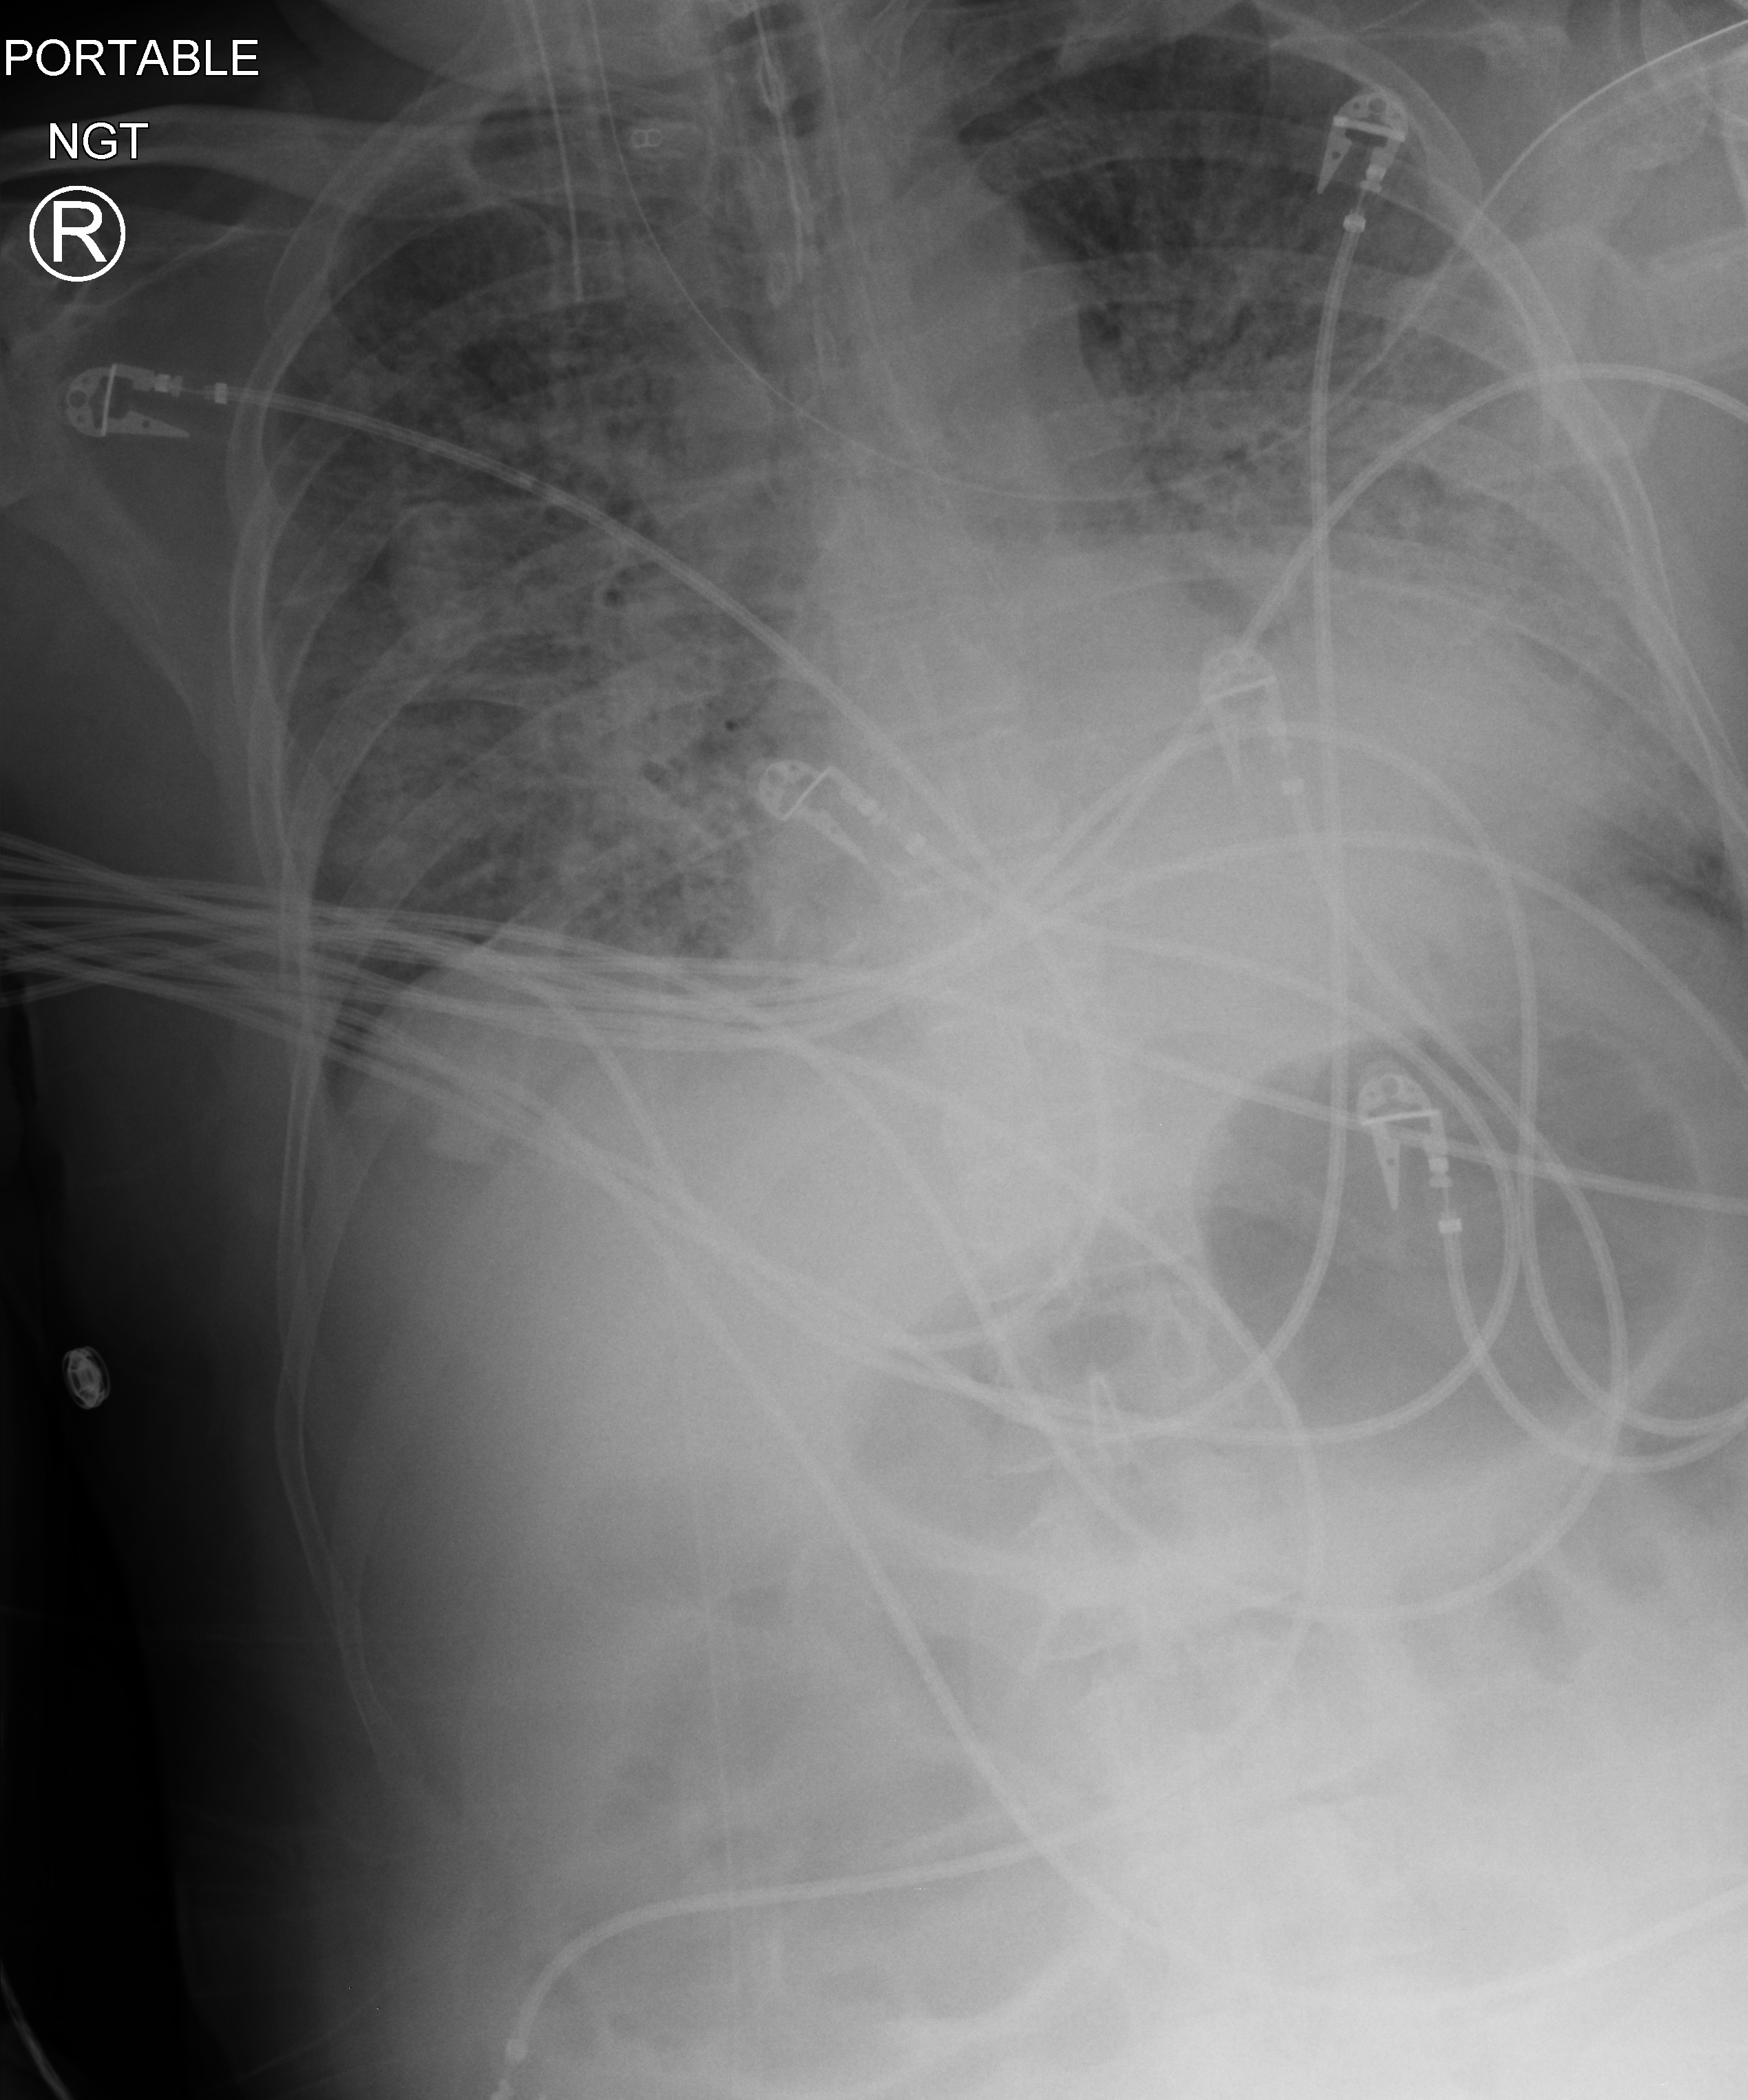
Chest X-ray (portable), anteroposterior (AP) projection. Patient hospitalised with COVID-19; male, aged 60–74 years.
Hospital-stay facts (about this admission, not read from this image; timing relative to this image not recorded): hypertension (admission record): yes; length of hospital stay: 28 days; diabetes (admission record): no.